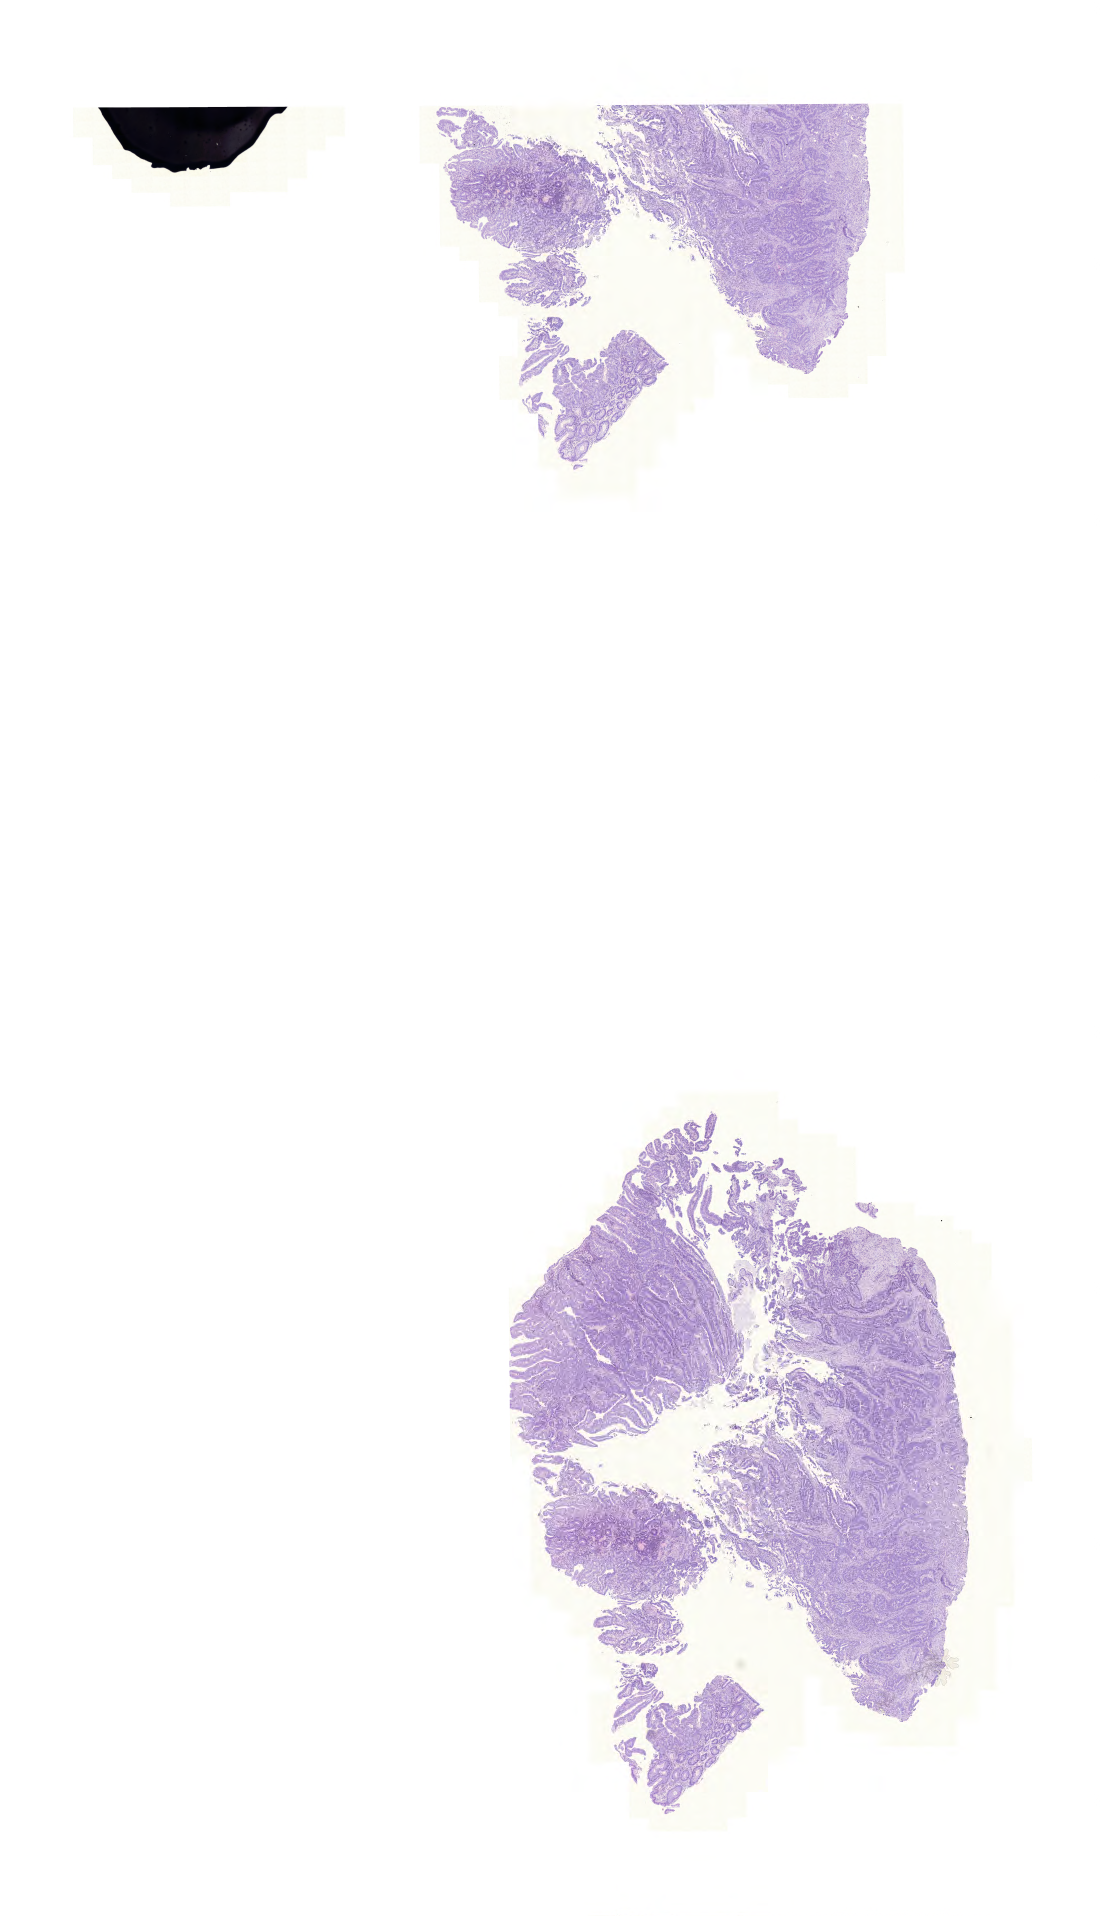
Digitized H&E tissue section (whole slide), shown as a low-resolution overview of the whole scanned area (about 16.4 x 28.5 mm). Formalin-fixed paraffin-embedded (FFPE) diagnostic section. Primary tumour sample from the rectum. Patient: female, age at initial diagnosis 66 years.
AJCC pathologic stage: IIIC (6th edition). Diagnosis: Adenocarcinoma, NOS (rectosigmoid junction). Lymph nodes positive (case pathology): 5 of 31 examined.